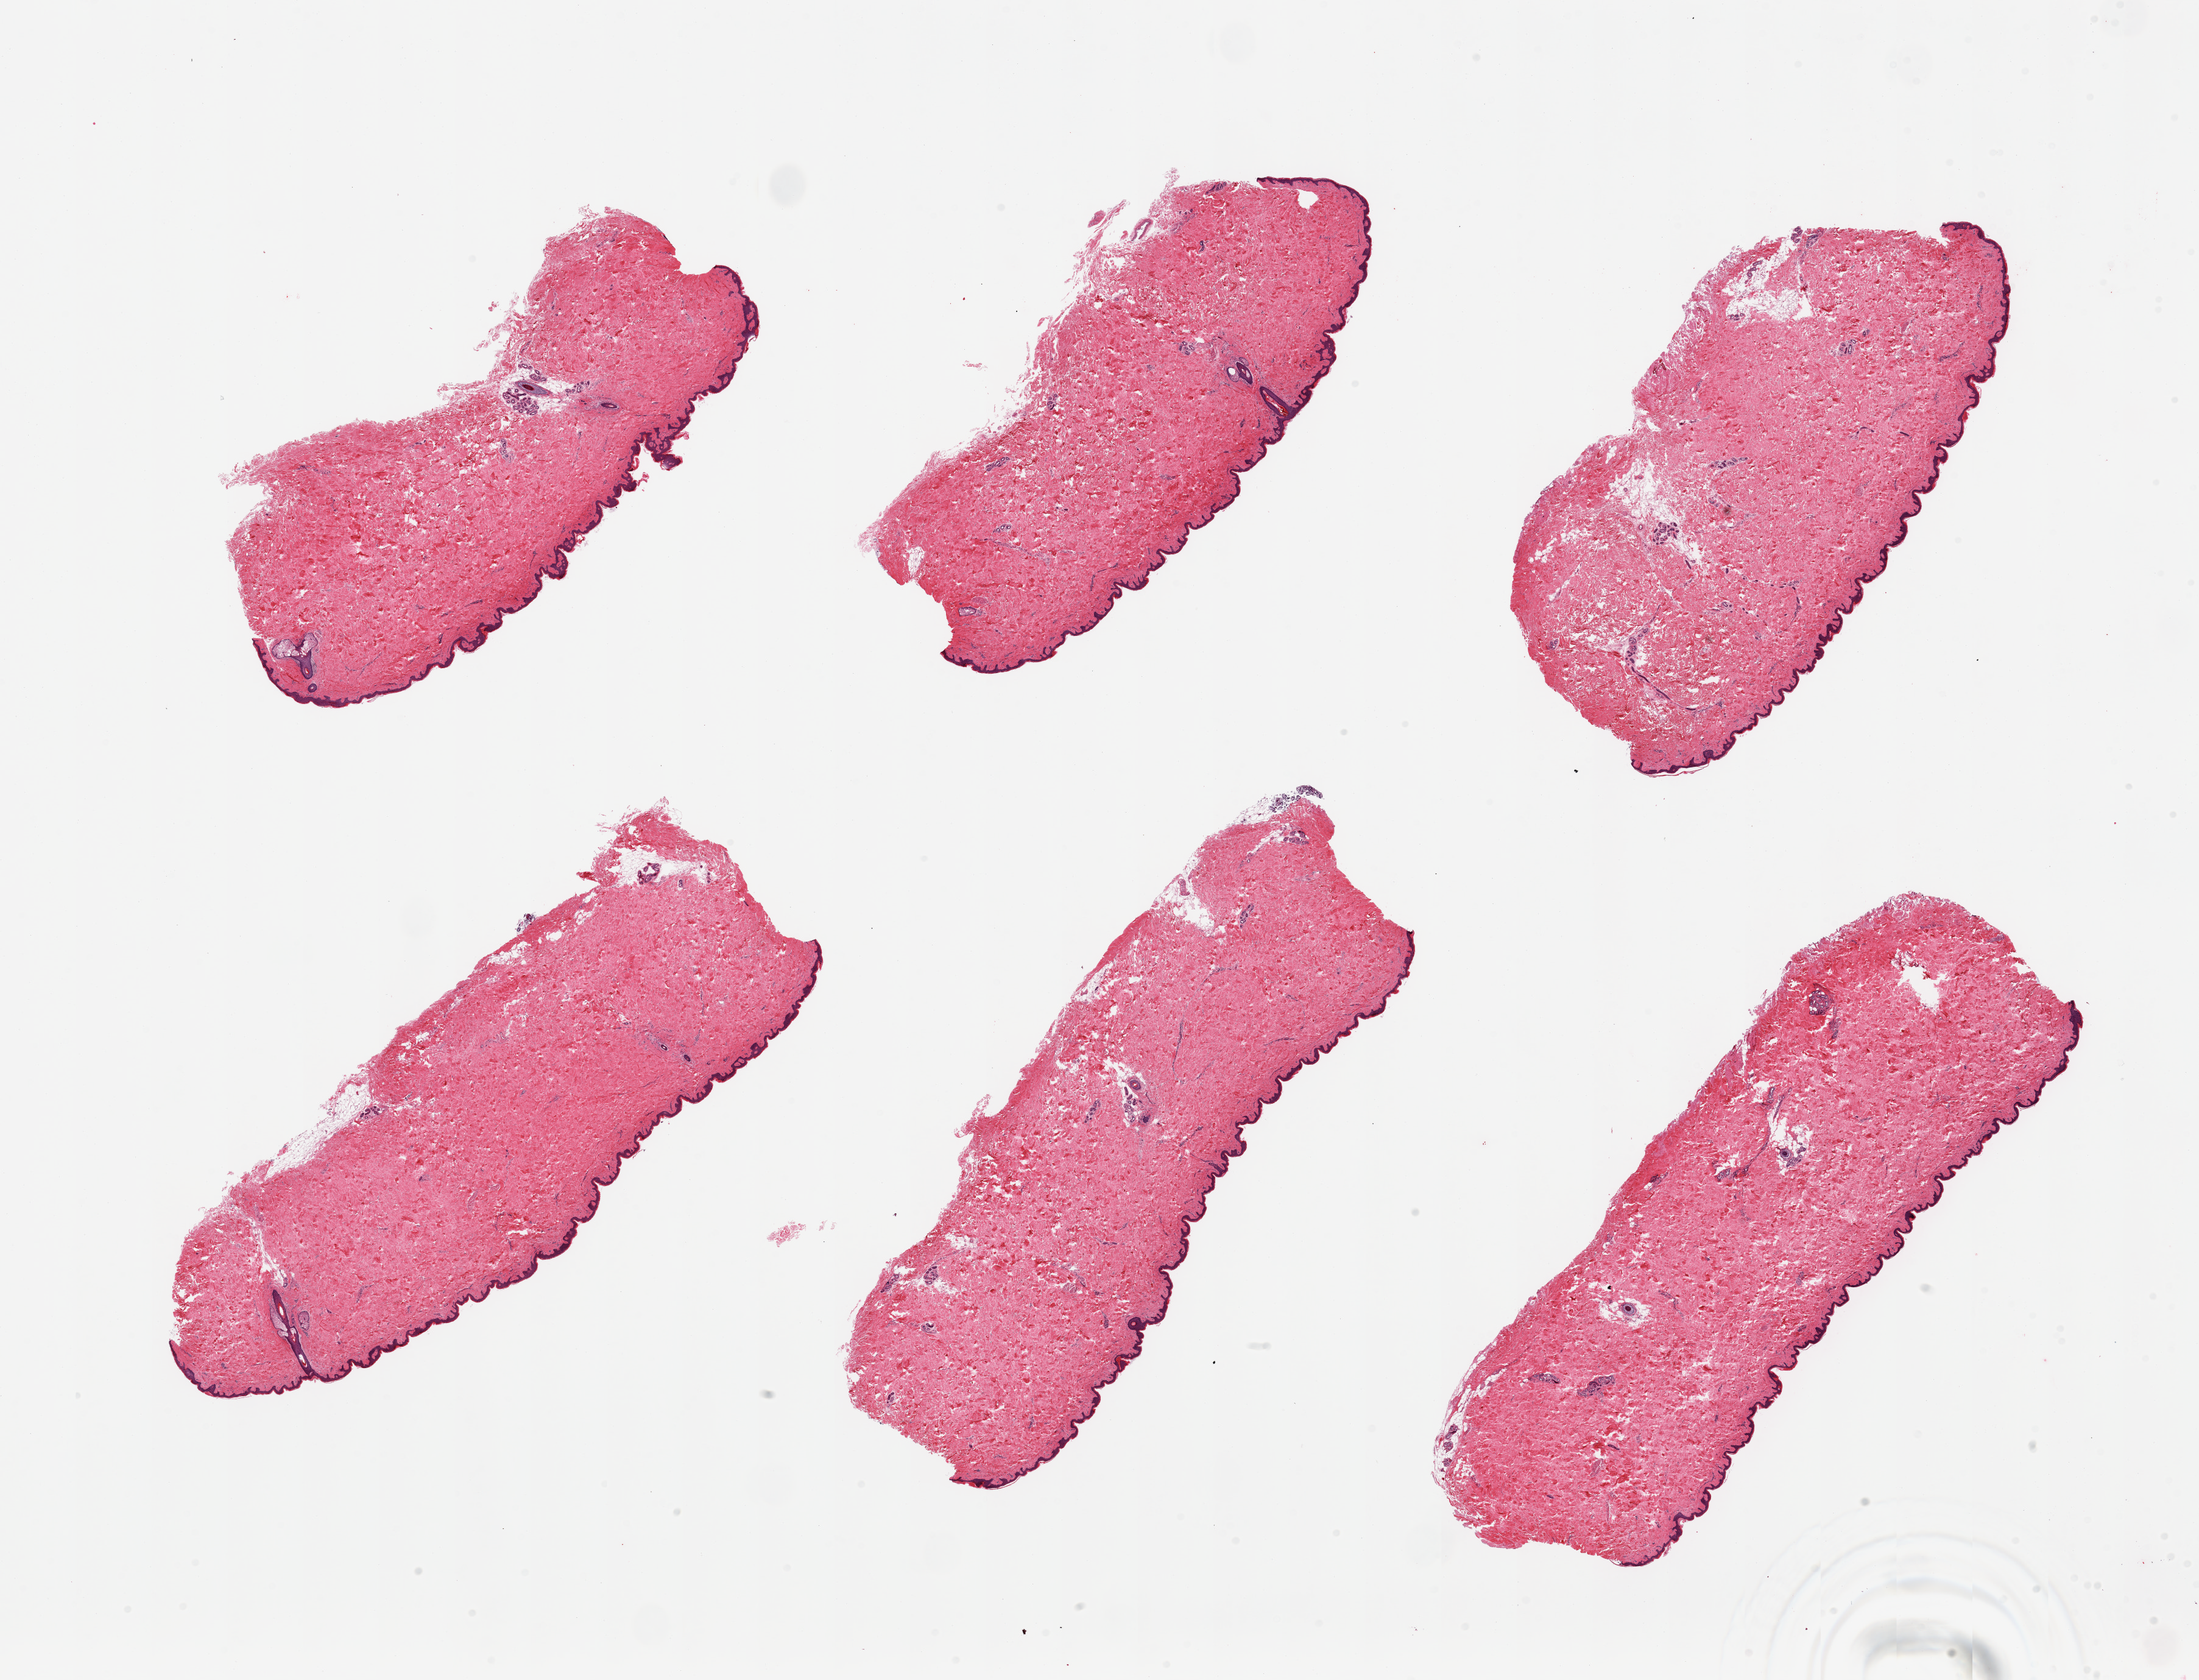
Digitized H&E-stained section, brightfield — shown as a low-resolution overview of the whole scanned area (about 28.5 x 21.8 mm), PAXgene-fixed paraffin-embedded (PFPE) section, sampled site (target tissue): skin of suprapubic region, donor tissue sample. Female donor.
* pathologist's review note for this sample: 6 pieces; well trimmed, but small carryover of intestinal glands